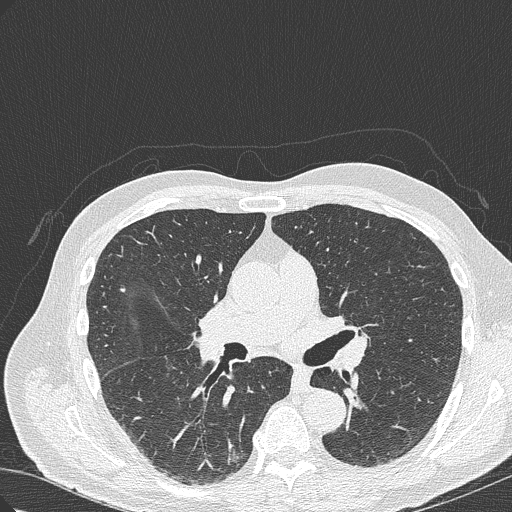
Low-dose screening chest CT, axial slice; baseline annual screen; lung window (W 1500 / L -600 HU); 1 mm slice thickness. Male, age 70 years at enrolment.
Lesion marked by an expert reader, bounding box (x1, y1, x2, y2) in pixels: (199, 419, 262, 476). The screening reader recorded 4 non-calcified nodules or masses ≥4 mm on this exam (right lower lobe, right lower lobe, right upper lobe, right lower lobe); which of them this box marks is not recorded. Lung cancer was diagnosed 978 days after this screen (after the third annual screen): bronchiolo-alveolar adenocarcinoma, NOS, right lower lobe, poorly differentiated (G3), stage IB (AJCC 6th edition), 30 mm at pathology.